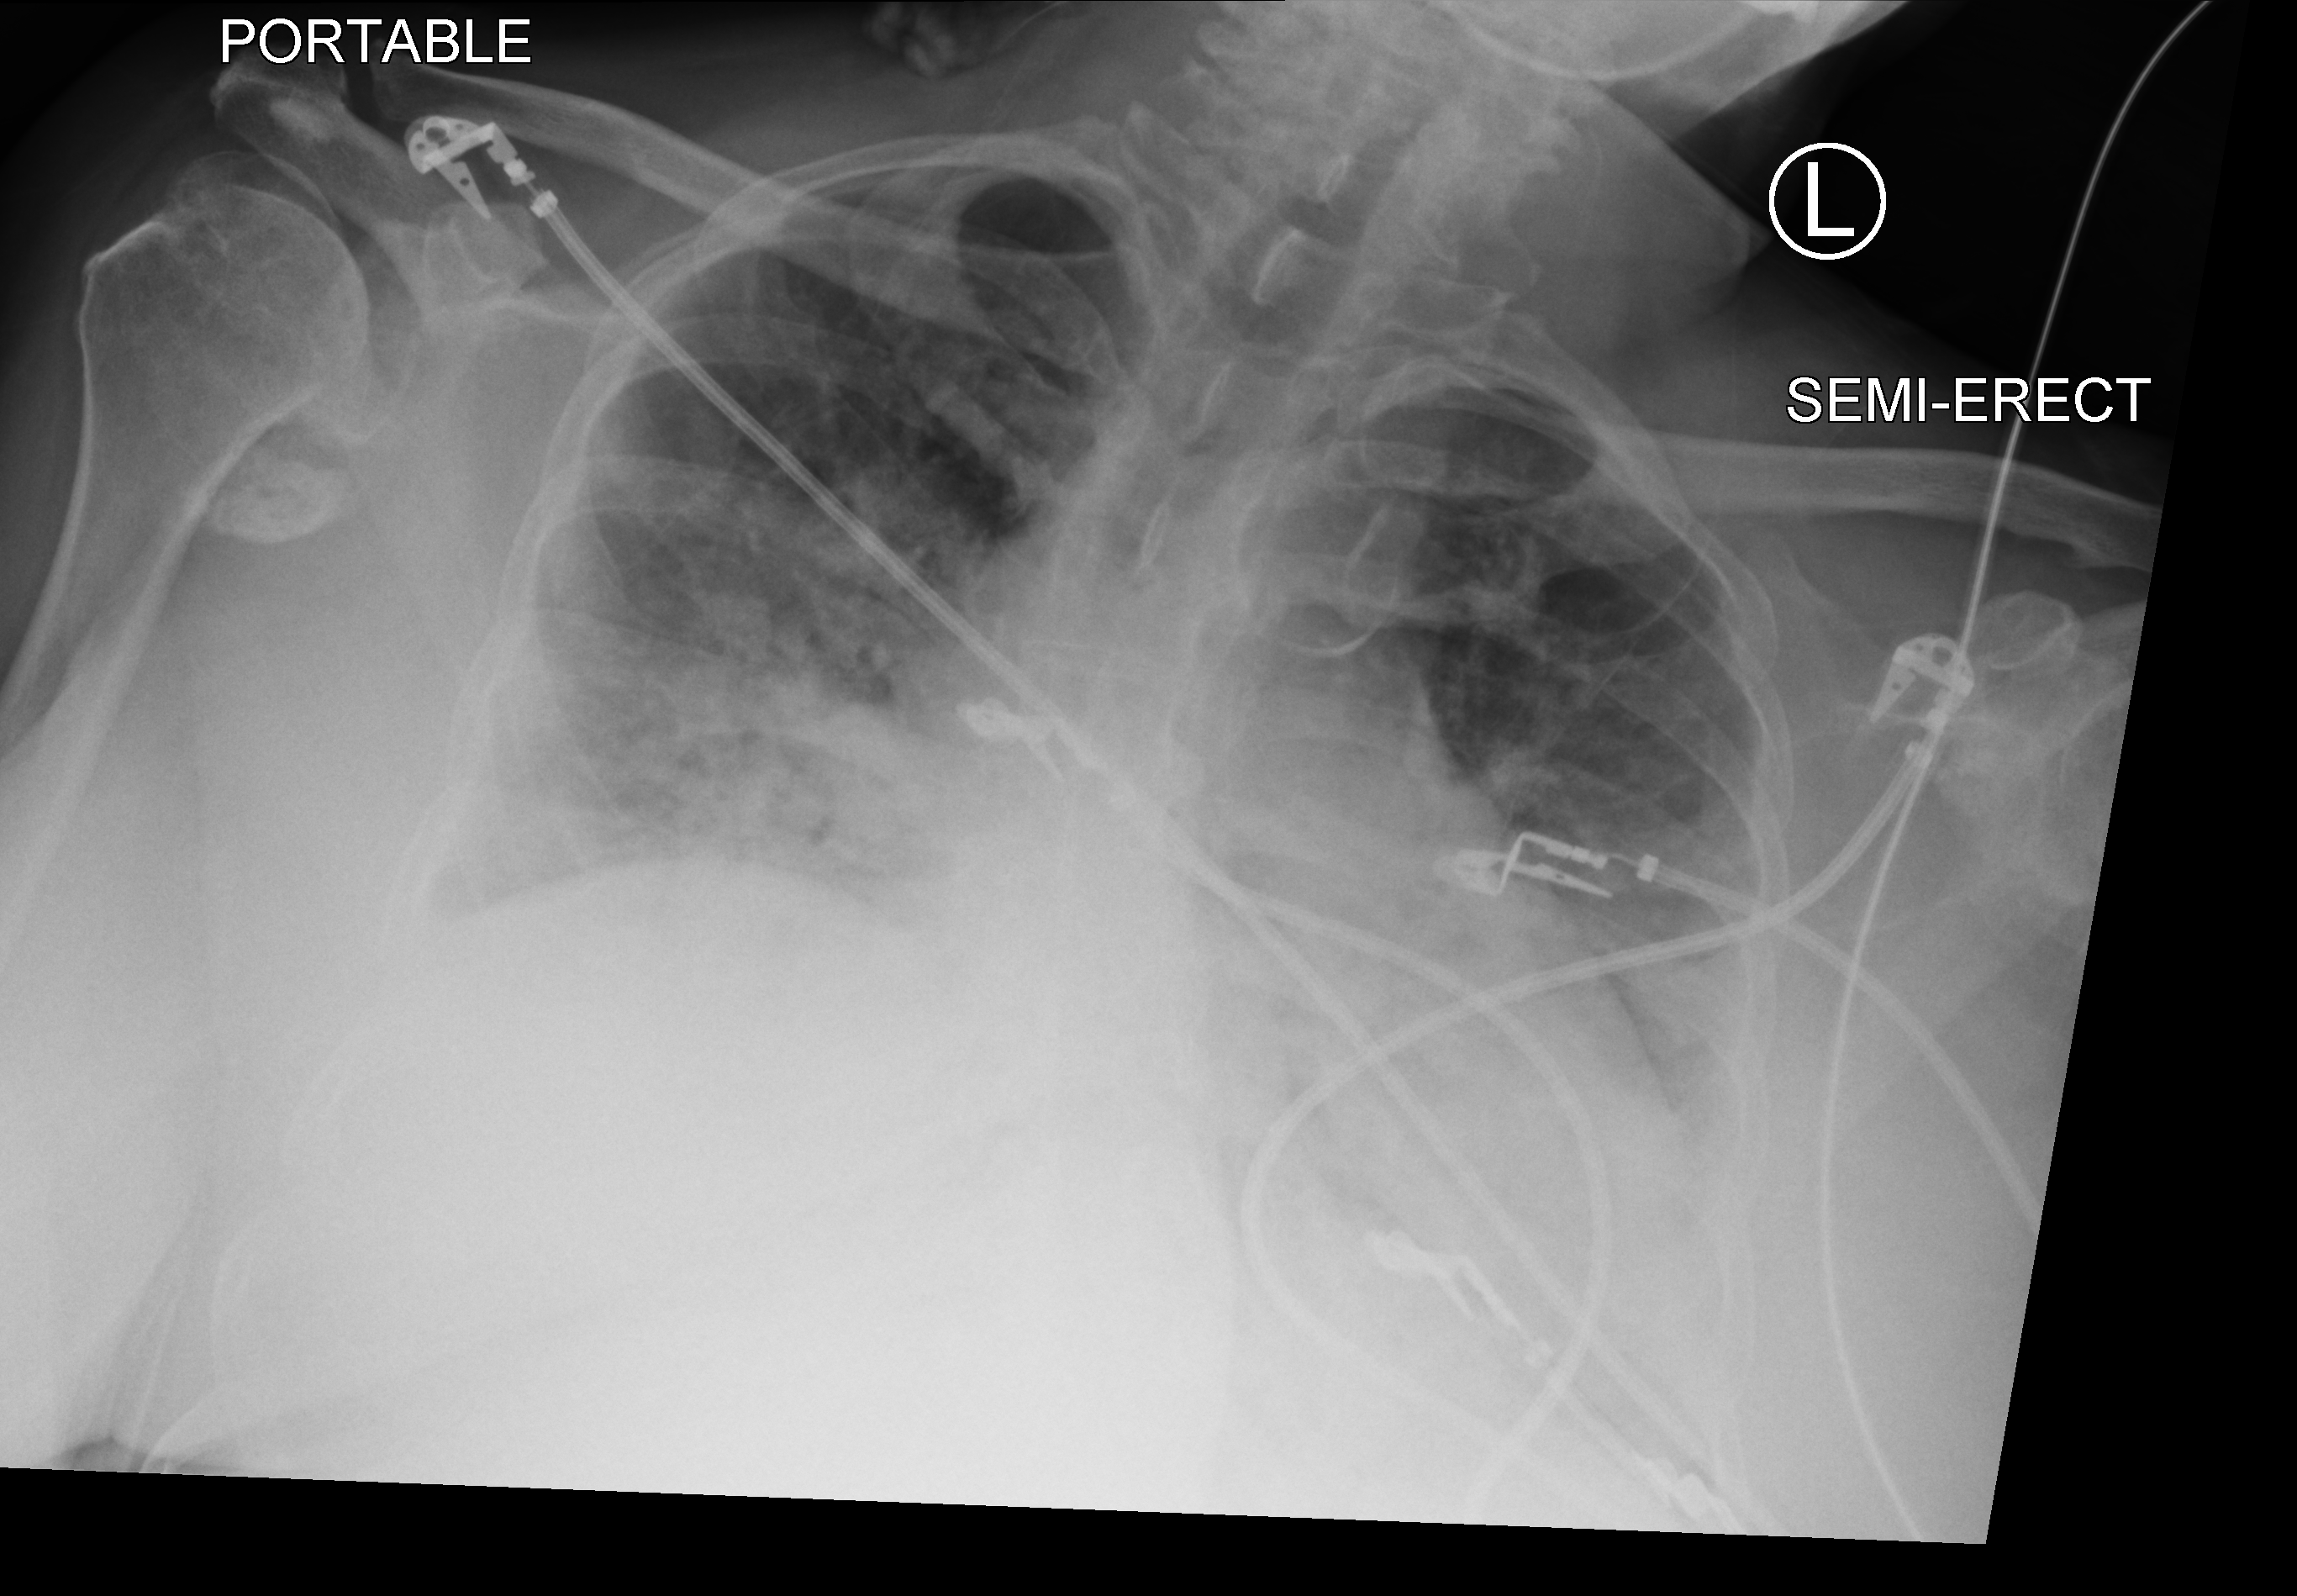
Bedside chest radiograph (computed radiography); anteroposterior (AP) projection. Patient hospitalised with COVID-19; female, aged 60–74 years.
Hospital-stay facts (about this admission, not read from this image; timing relative to this image not recorded):
- hypertension (admission record): yes
- admitted to intensive care during this hospital stay: yes